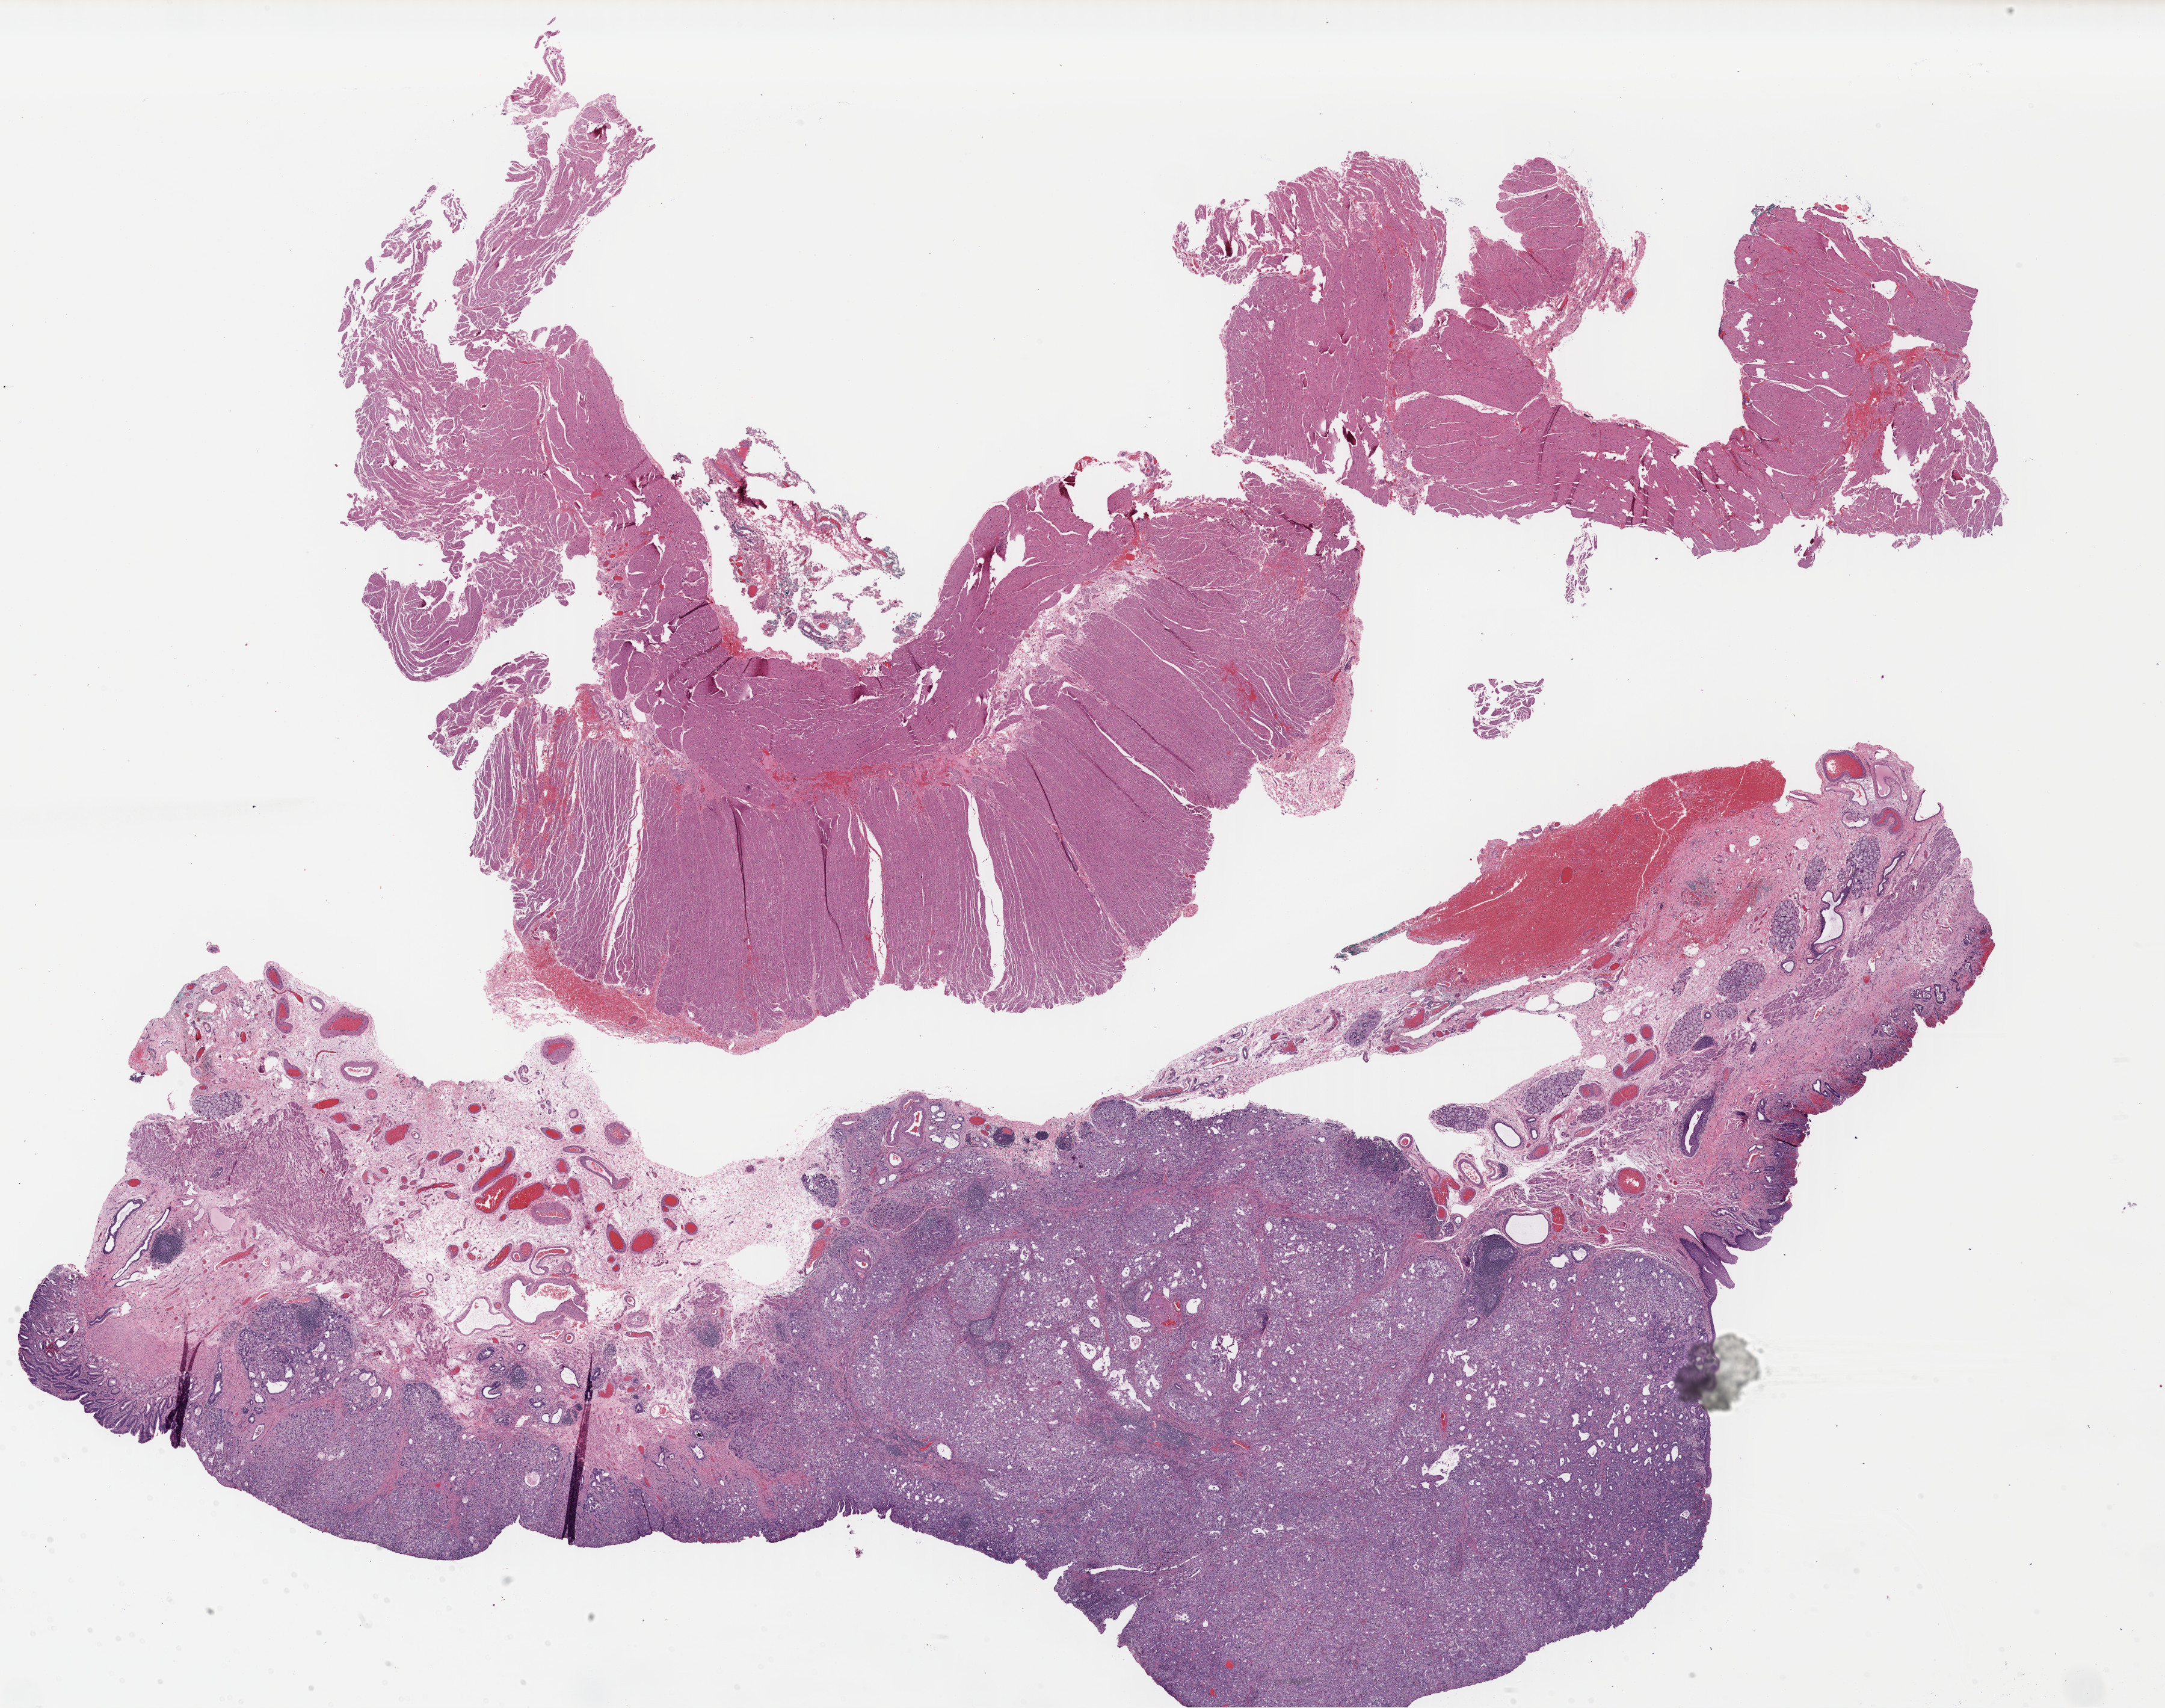
Whole-slide histology image, H&E — low-resolution overview of the scanned area, about 28.3 x 22.3 mm (from a 40x scan). Formalin-fixed paraffin-embedded (FFPE) diagnostic section. Primary tumour sample from the esophagus. Patient: male, age at initial diagnosis 63 years. Histologic grade: G3 (poorly differentiated).
• AJCC pathologic stage: IIB (7th edition)
• lymph nodes positive (case pathology): 1 of 18 examined
• pathologic diagnosis: Adenocarcinoma, NOS (lower third of esophagus)